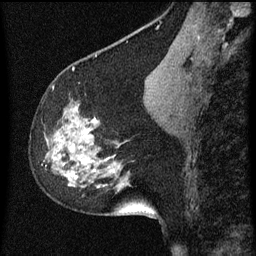
Breast MRI (dynamic contrast-enhanced), one sagittal slice; slice 26 of 60 in the series (ordered by position); dynamic contrast-enhanced series, image 2 of 3 at this slice position (ordered by acquisition); 1.5 T; TE 4.2 ms, TR 8 ms; 2 mm slice thickness; 256 × 256 image matrix. Patient: female, 61 years.
Annotated regions visible in this slice (semi-automatic segmentation, software-assisted and operator-edited):
- analysis volume of interest (the breast-tissue region the enhancement analysis was run in; not a lesion): box from (x=42, y=86) to (x=139, y=209) px
- tumour enhancement mask (voxels above the 70 % enhancement threshold inside the analysis volume of interest): (x=55, y=160)–(x=78, y=179)